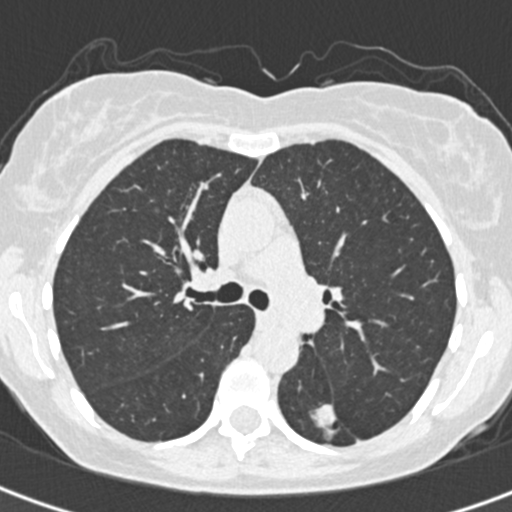
Low-dose screening chest CT, one axial slice; reconstruction kernel B30f; lung window (W 1500 / L -600 HU); 512 × 512 image matrix.
Annotated regions visible in this slice (outlined manually by an expert reader):
- lesion 1 (tumor, lower lobe of left lung): bounding box (x1, y1, x2, y2) in pixels: (312, 404, 336, 436)